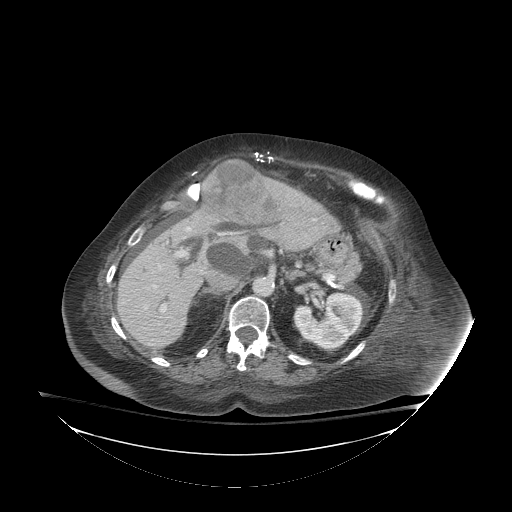
Contrast-enhanced abdominal CT (liver protocol), one axial slice. Position 49 of 81 along the scan axis. 140 kVp. Soft-tissue window (W 400 / L 40 HU). 2.5 mm slice thickness. 512 × 512 image matrix, field of view 500 × 500 mm. Case-level facts recorded for this patient, not image findings: diagnosis: hepatocellular carcinoma (patient treated with transarterial chemoembolisation; whether this scan precedes or follows treatment is not stated here); TNM stage (as recorded): Stage-I; Child-Pugh class: B; tumour differentiation: well-moderately differentiated; tumour nodularity: uninodular.
Structures marked on this image (semi-automatically segmented with operator editing):
- liver parenchyma outside the tumour (the mass and vessels are separate outlines, so this box may not span the whole liver): box from (x=116, y=178) to (x=334, y=348) px
- mass: (x=201, y=158)–(x=280, y=224)
- liver vessels: (x=145, y=227)–(x=191, y=312)